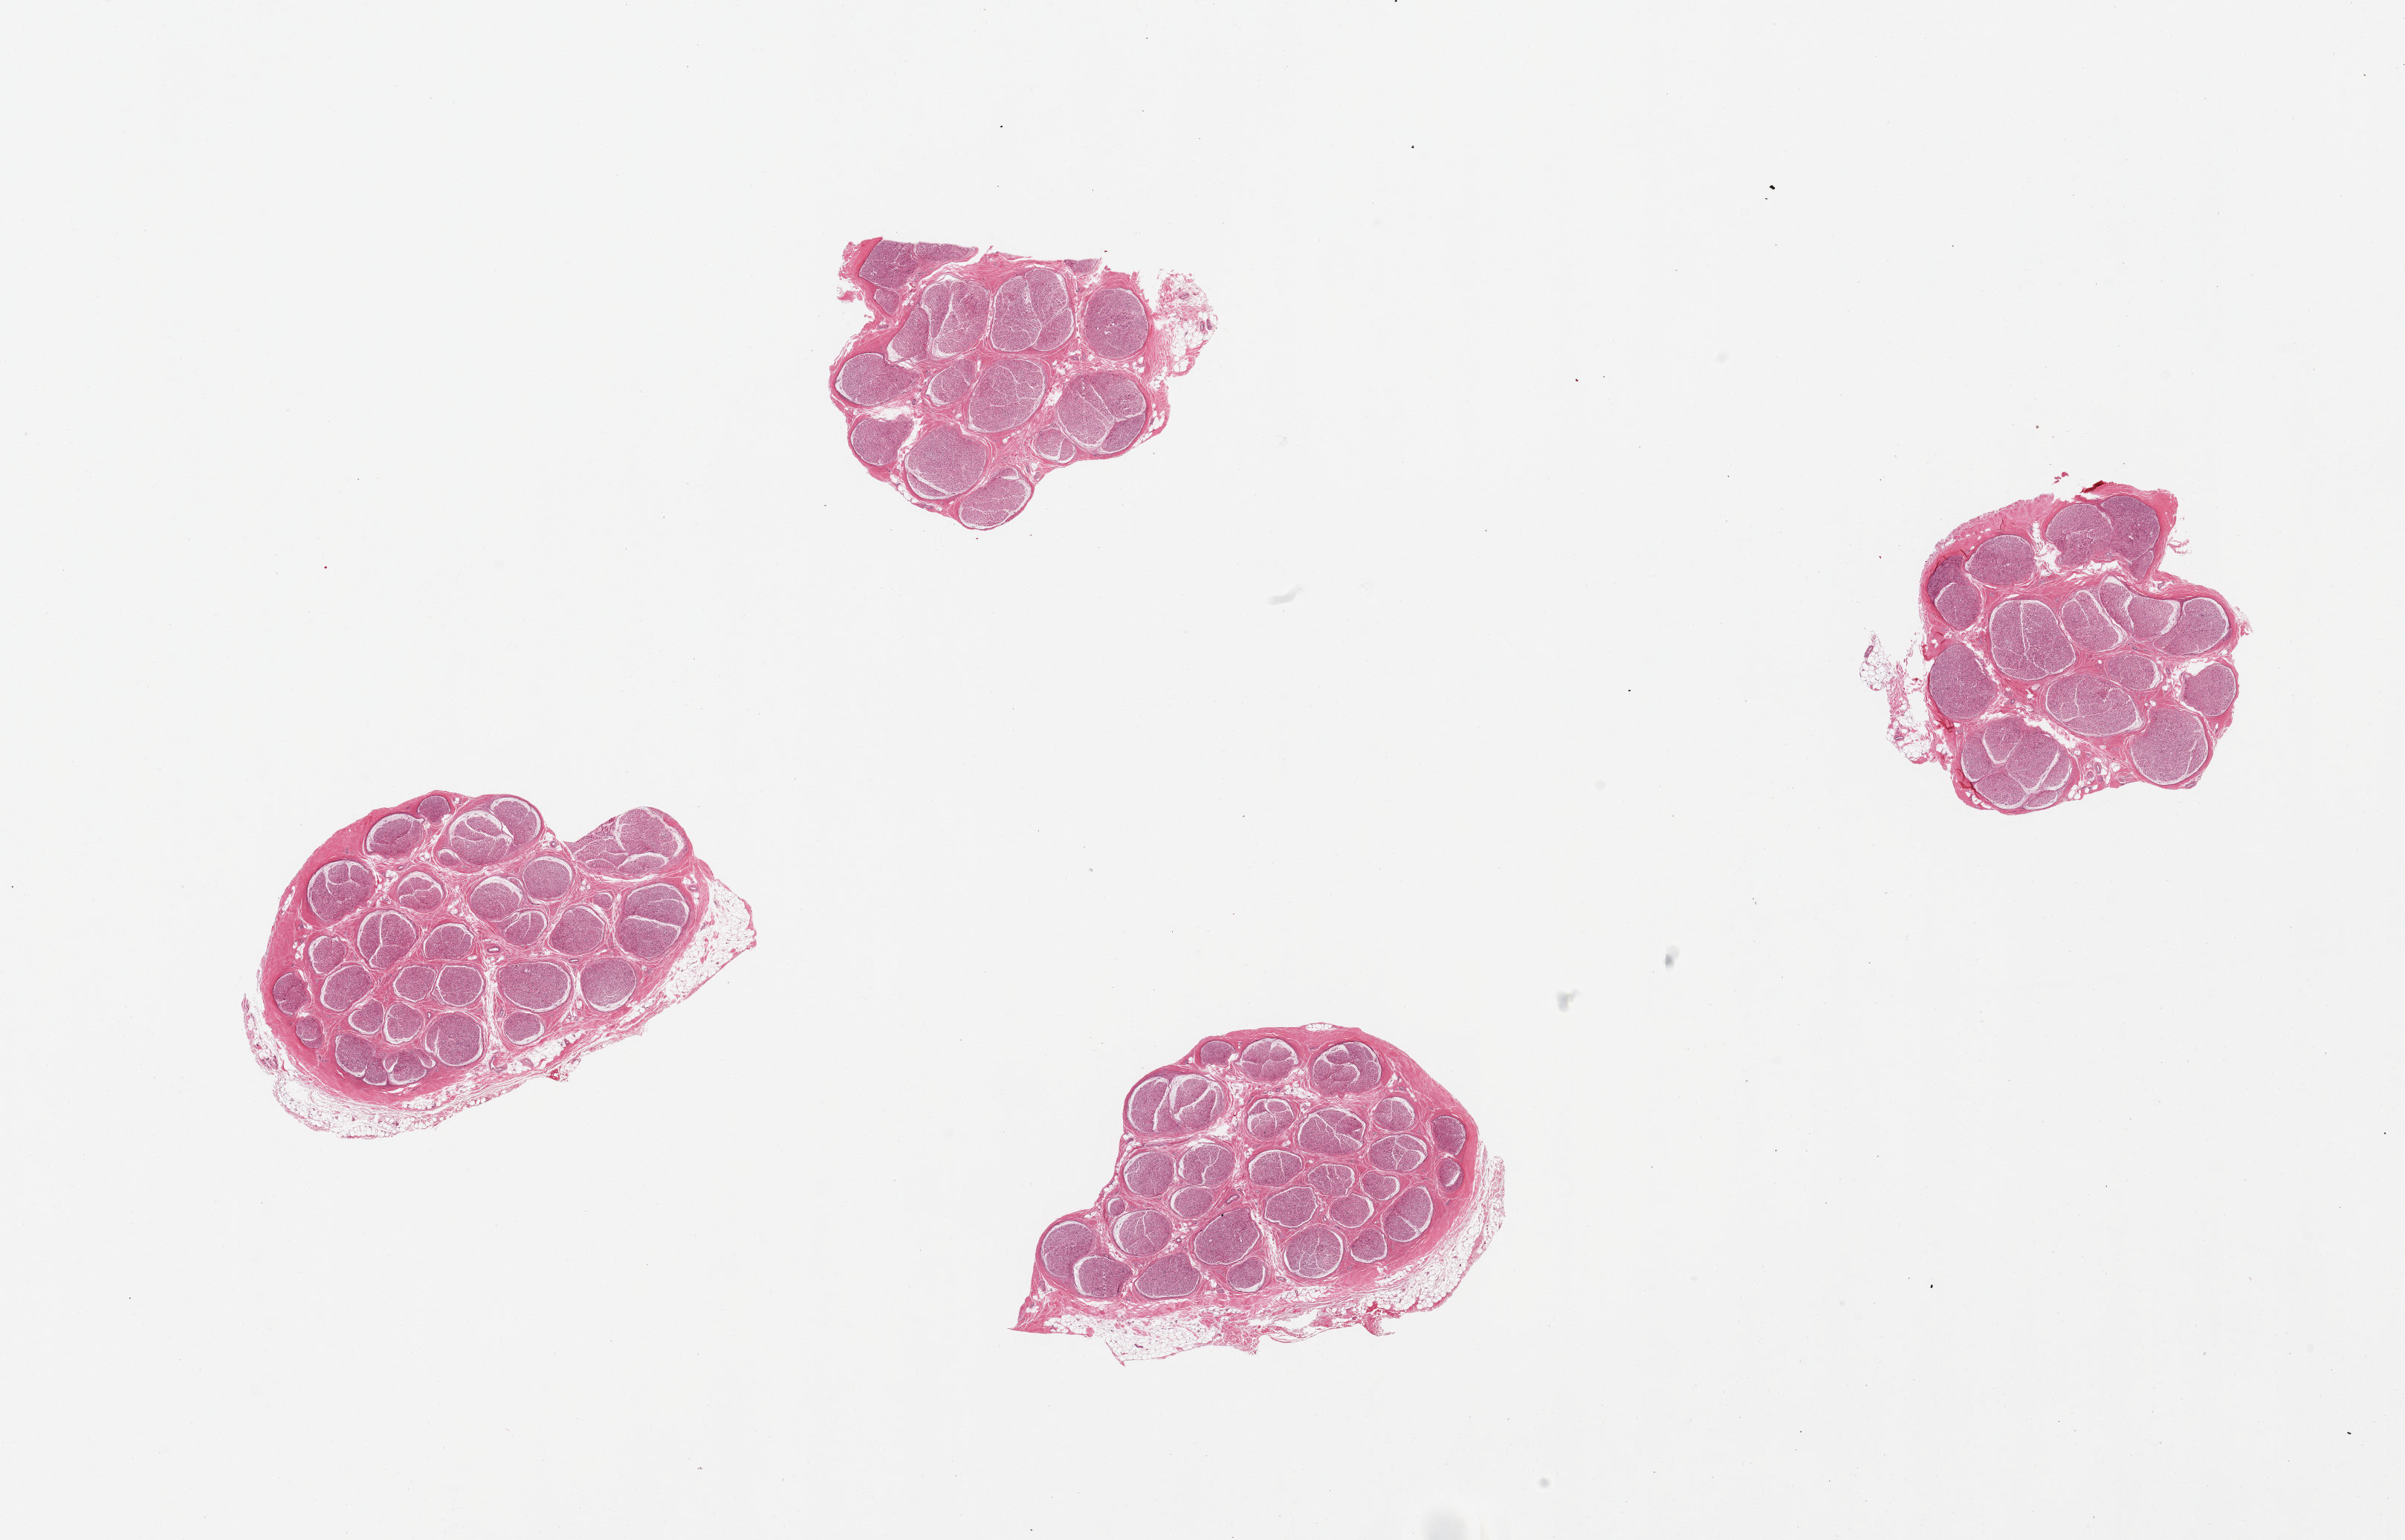
Whole-slide image, H&E stain, brightfield, a low-resolution overview of the entire scanned area, about 25.6 x 16.4 mm (from a 20x scan). PAXgene-fixed, paraffin-embedded tissue. Sampled site (target tissue): tibial nerve. Tissue donor sample. Donor: female.
Pathologist's review note for this sample: 4 pieces, up to 10% attached adipose tissue.